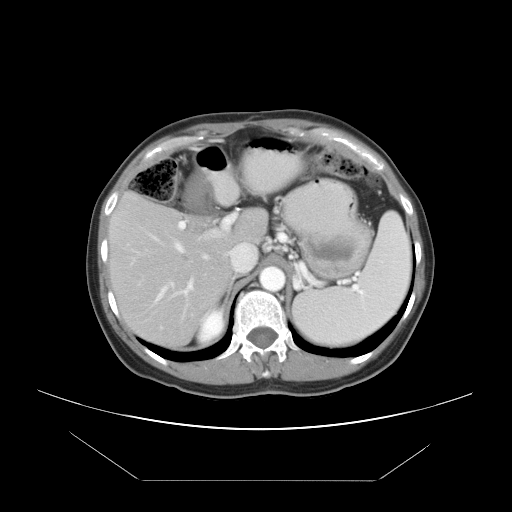
Contrast-enhanced abdominal CT, one axial slice; slice 31 of 45 in the series (ordered by position); reconstruction kernel STANDARD; 120 kVp; intravenous contrast given; soft-tissue window (W 400 / L 40 HU); 5 mm slice thickness; 512 × 512 image matrix. Female patient, age 52 years. Case-level facts recorded for this patient, not image findings: diagnosis: colorectal cancer liver metastases, imaged before liver resection; multiple liver metastases: yes; largest metastasis: 2.5 cm; disease in both lobes: no.
Annotated regions visible in this slice (expert manual segmentation):
- hepatic veins: box from (x=130, y=227) to (x=186, y=303) px
- liver: (x=111, y=195)–(x=267, y=346)
- planned liver remnant (the part of the liver to remain after resection): (x=111, y=195)–(x=267, y=333)
- portal vein (with intrahepatic branches): (x=176, y=214)–(x=233, y=296)